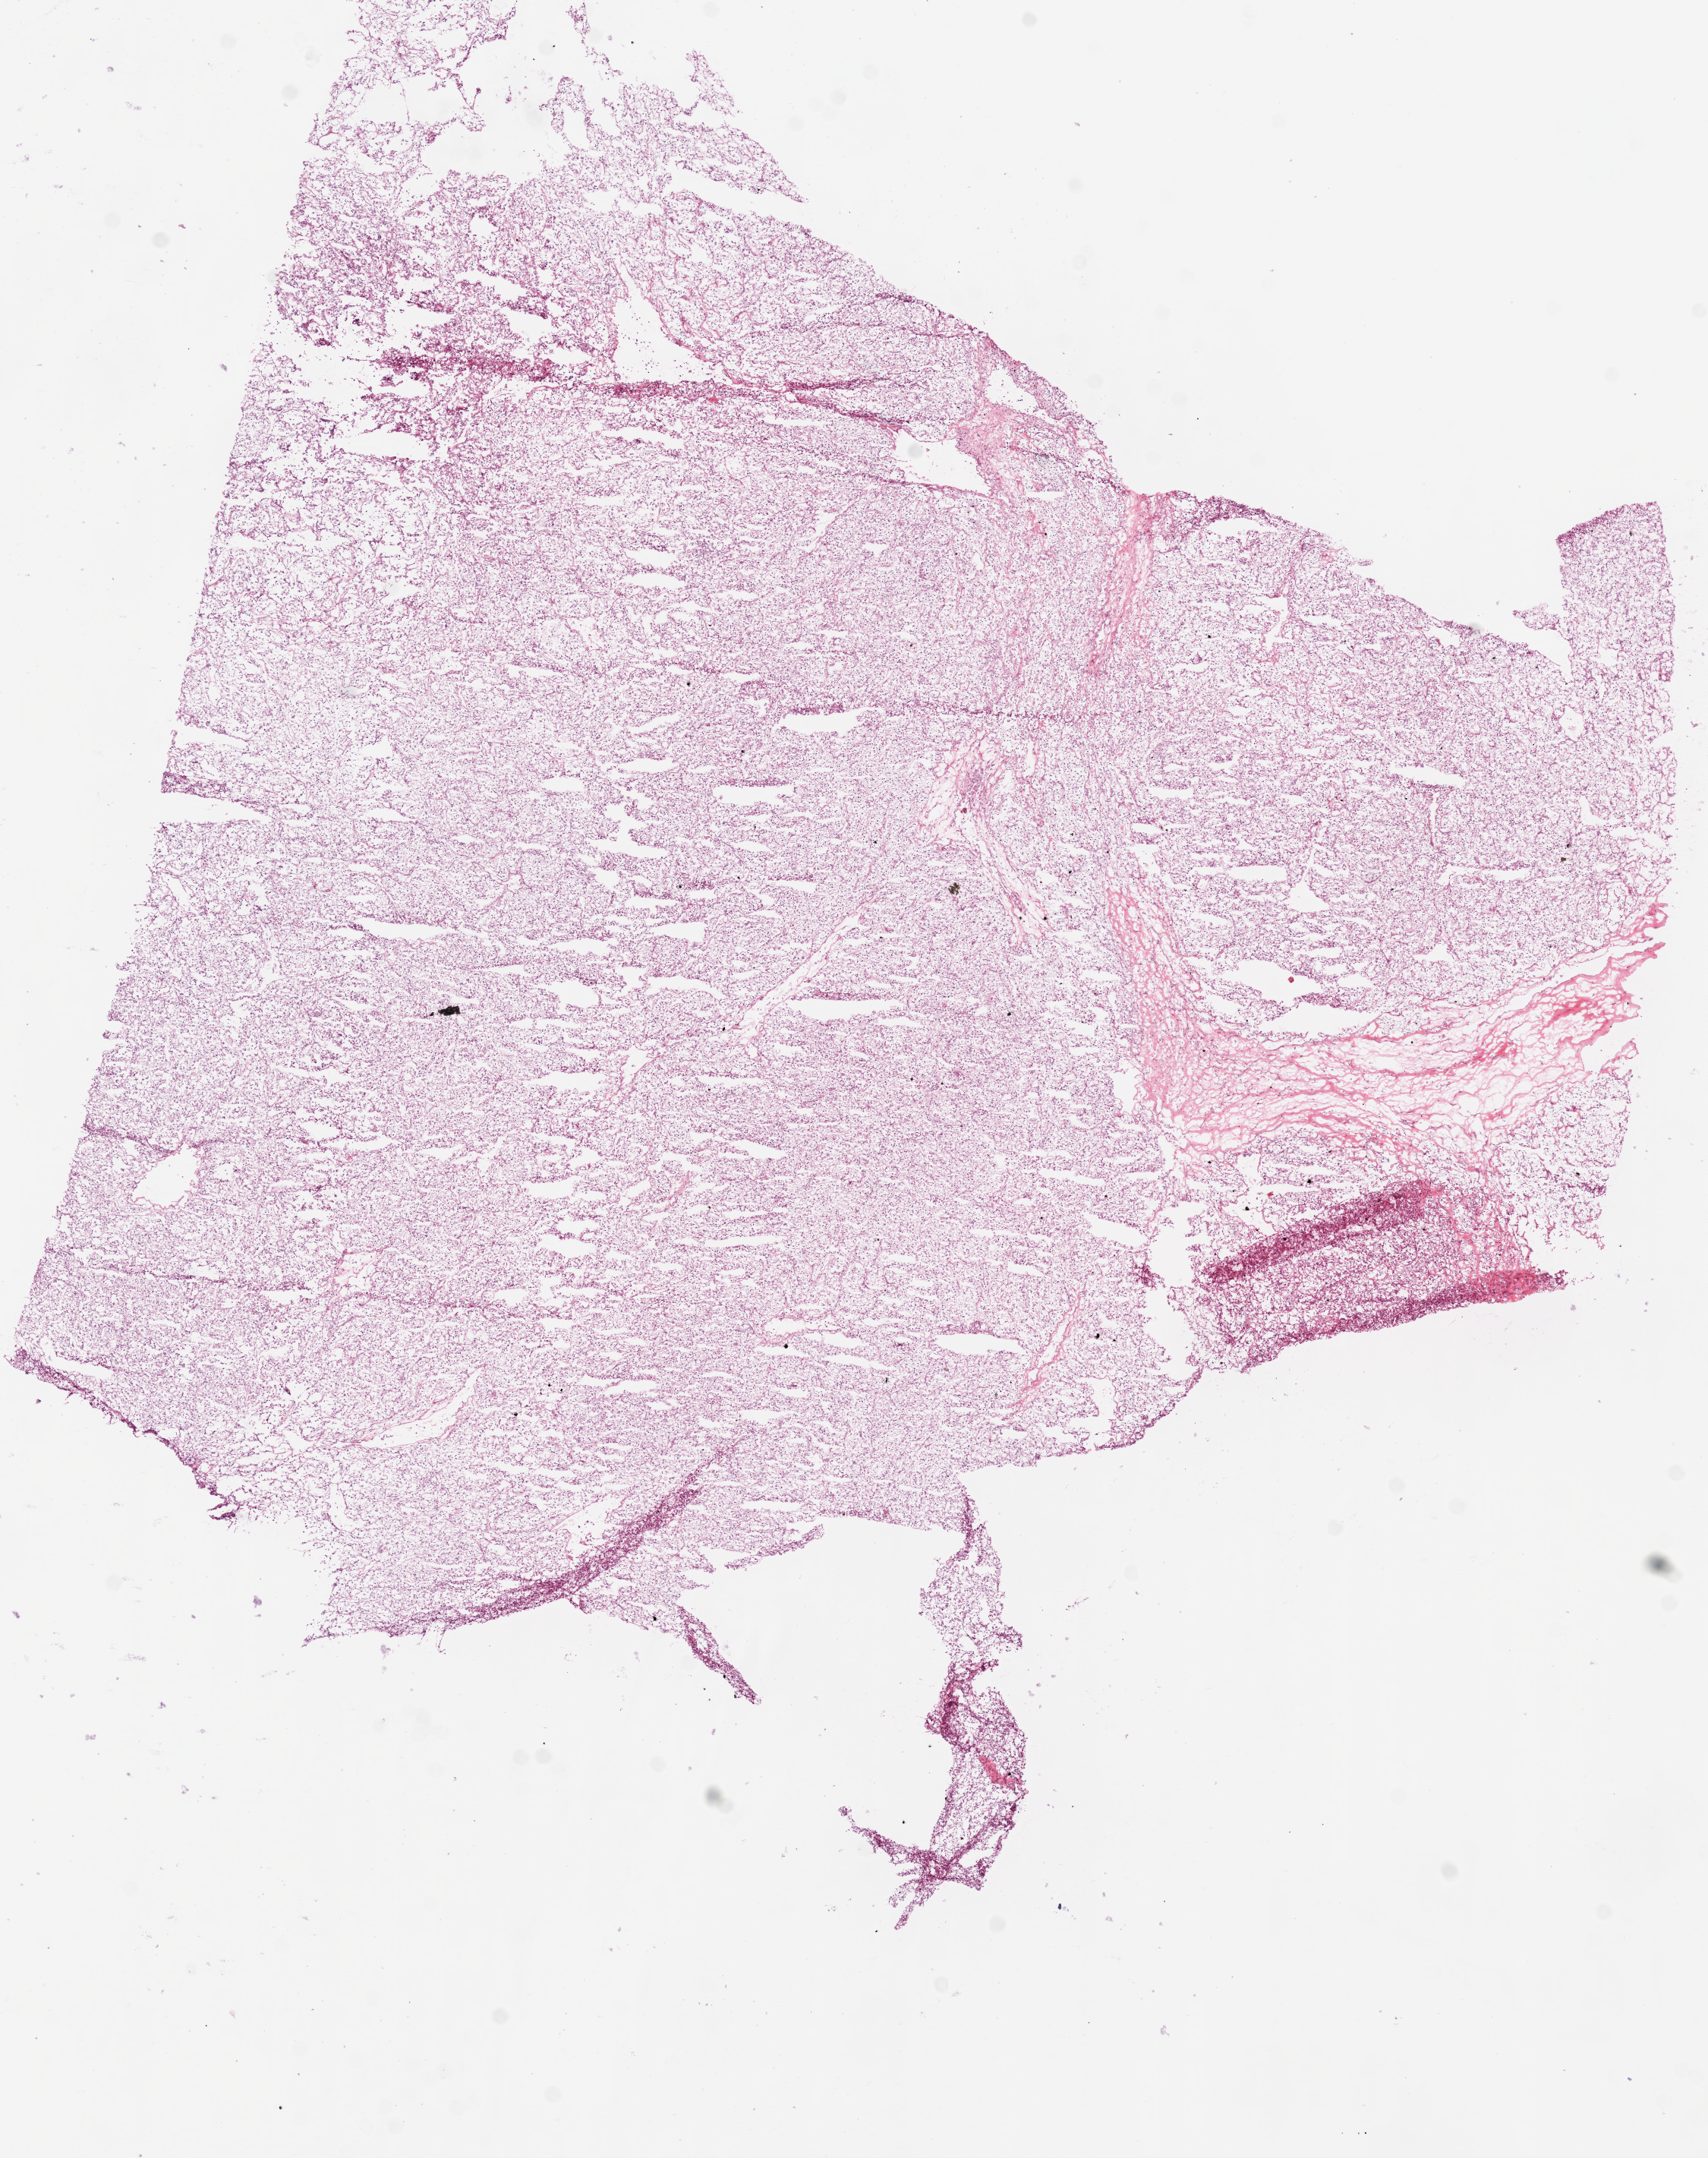
Digitized Hematoxylin and eosin (H&E) stained tissue section (whole slide) — shown as a low-resolution overview of the whole scanned area (about 9.0 x 11.4 mm, slide scanned at 20x). Frozen section from the bottom of the tissue portion. Kidney, primary tumour sample. Male patient; age at initial diagnosis 57 years. Histologic grade: G3 (poorly differentiated). Slide review estimates, as recorded: tumour cells 85%, tumour nuclei 85%, normal cells 0%, stromal cells 15%, necrosis 0%.
- AJCC pathologic stage: IV (7th edition)
- histologic diagnosis: Clear cell adenocarcinoma, NOS
- laterality: left